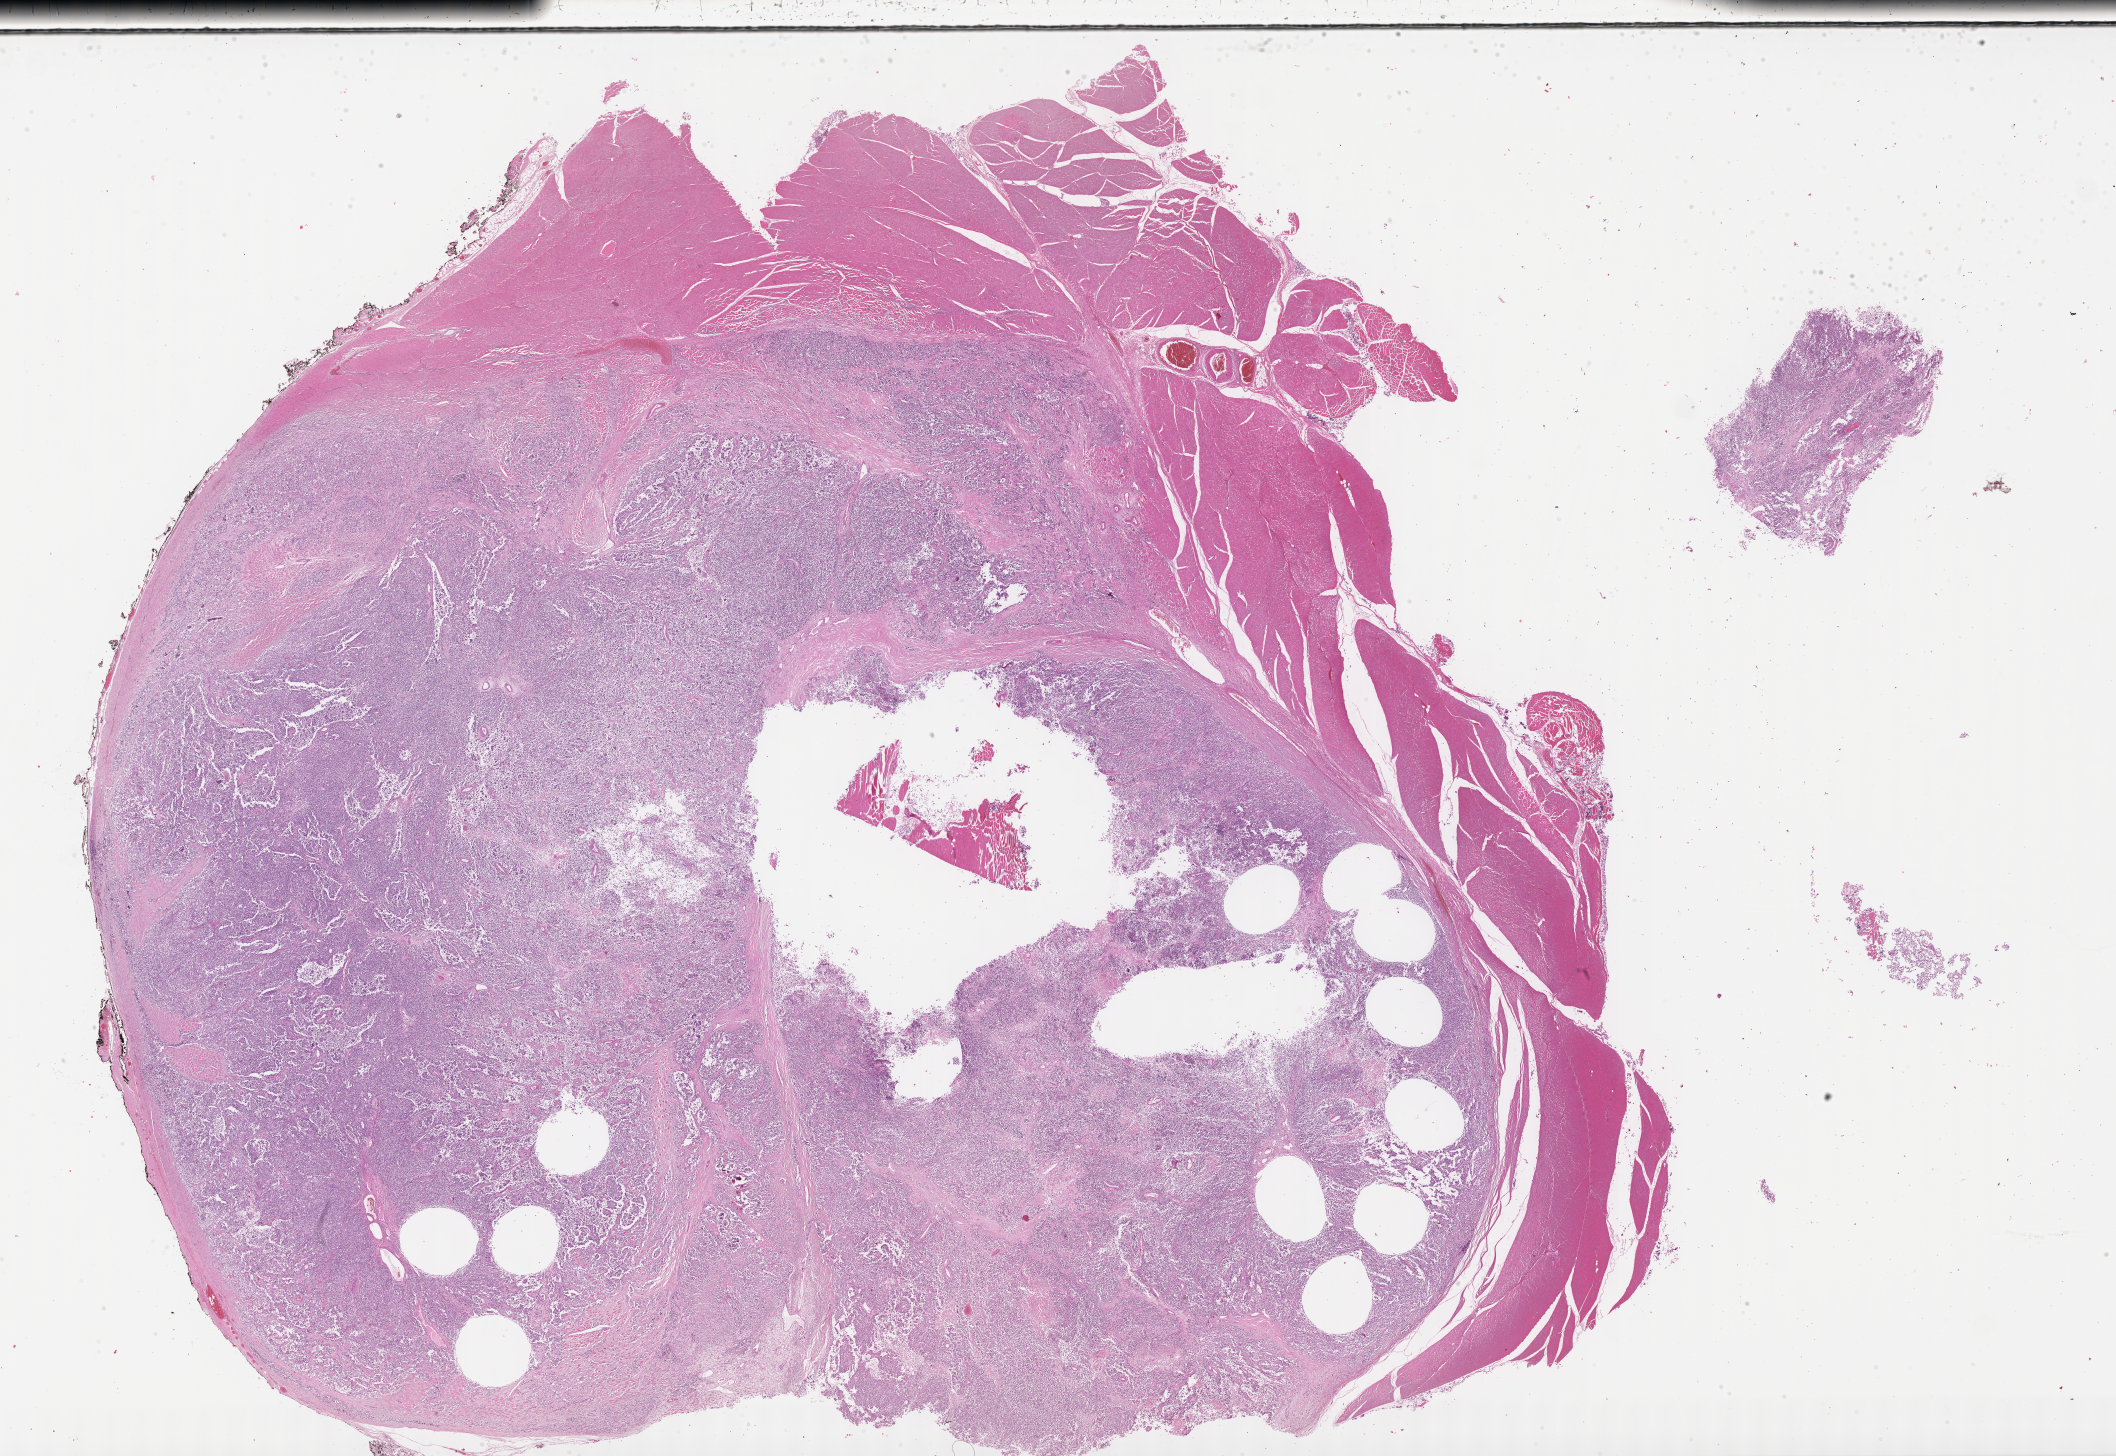
H&E whole-slide image of tumor tissue — a low-resolution overview of the entire scanned area, about 34.2 x 23.5 mm; FFPE section; sample anatomic site: thigh, right. Patient: male, age 6.8 years at diagnosis.
- metastatic status at presentation (as recorded): non-metastatic
- stage (as recorded): 2
- diagnosis: rhabdomyosarcoma; histological classification: alveolar rhabdomyosarcoma